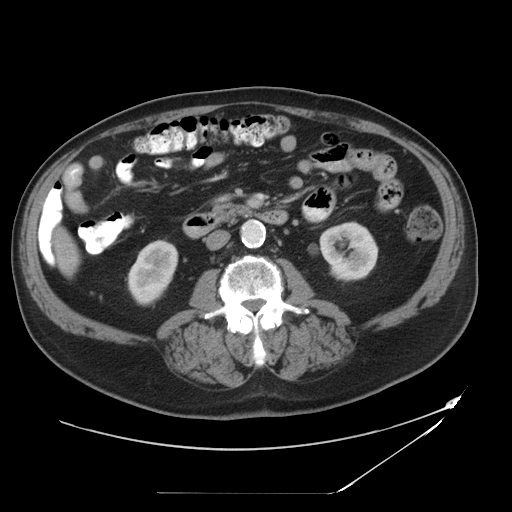
Contrast-enhanced abdominal CT, one axial slice. Position 11 of 49 along the scan axis. Reconstruction kernel STANDARD. Intravenous contrast given. Soft-tissue window (W 400 / L 40 HU). 5 mm slice thickness. 512 × 512 image matrix, field of view 461 × 461 mm. Male patient, age 72 years. From the clinical record (not read from this slice): diagnosis: colorectal cancer liver metastases, imaged before liver resection; multiple liver metastases: no; largest metastasis: 2.5 cm; disease in both lobes: no.
Outlined on this slice (manually delineated by an expert):
- liver: bounding box [x1, y1, x2, y2] px = [57, 233, 77, 274]
- planned liver remnant (the part of the liver to remain after resection): [57, 233, 76, 274]